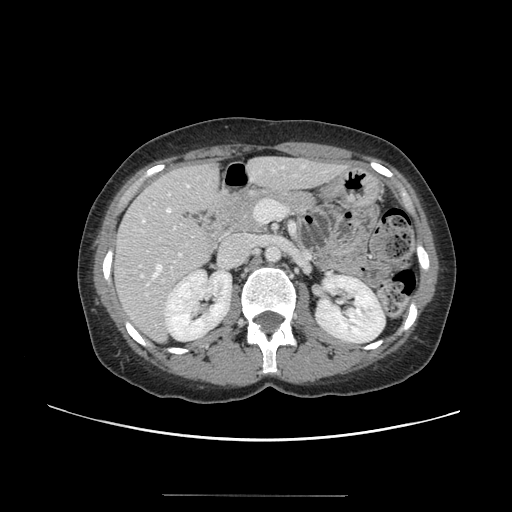
Contrast-enhanced abdominal CT, one axial slice. Slice 69 of 144 in the series (ordered by position). 120 kVp. Intravenous contrast given. Soft-tissue window (W 400 / L 40 HU). 512 × 512 image matrix, field of view 380 × 380 mm. Female patient, age 53 years. From the clinical record (not read from this slice): diagnosis: colorectal cancer liver metastases, imaged before liver resection; multiple liver metastases: yes; largest metastasis: 1.1 cm; disease in both lobes: no.
Structures marked on this image (manually delineated by an expert):
- hepatic veins: bounding box (x1, y1, x2, y2) in pixels: (141, 186, 189, 277)
- liver: (117, 159, 338, 341)
- planned liver remnant (the part of the liver to remain after resection): (117, 159, 324, 303)
- portal vein (with intrahepatic branches): (139, 200, 287, 296)